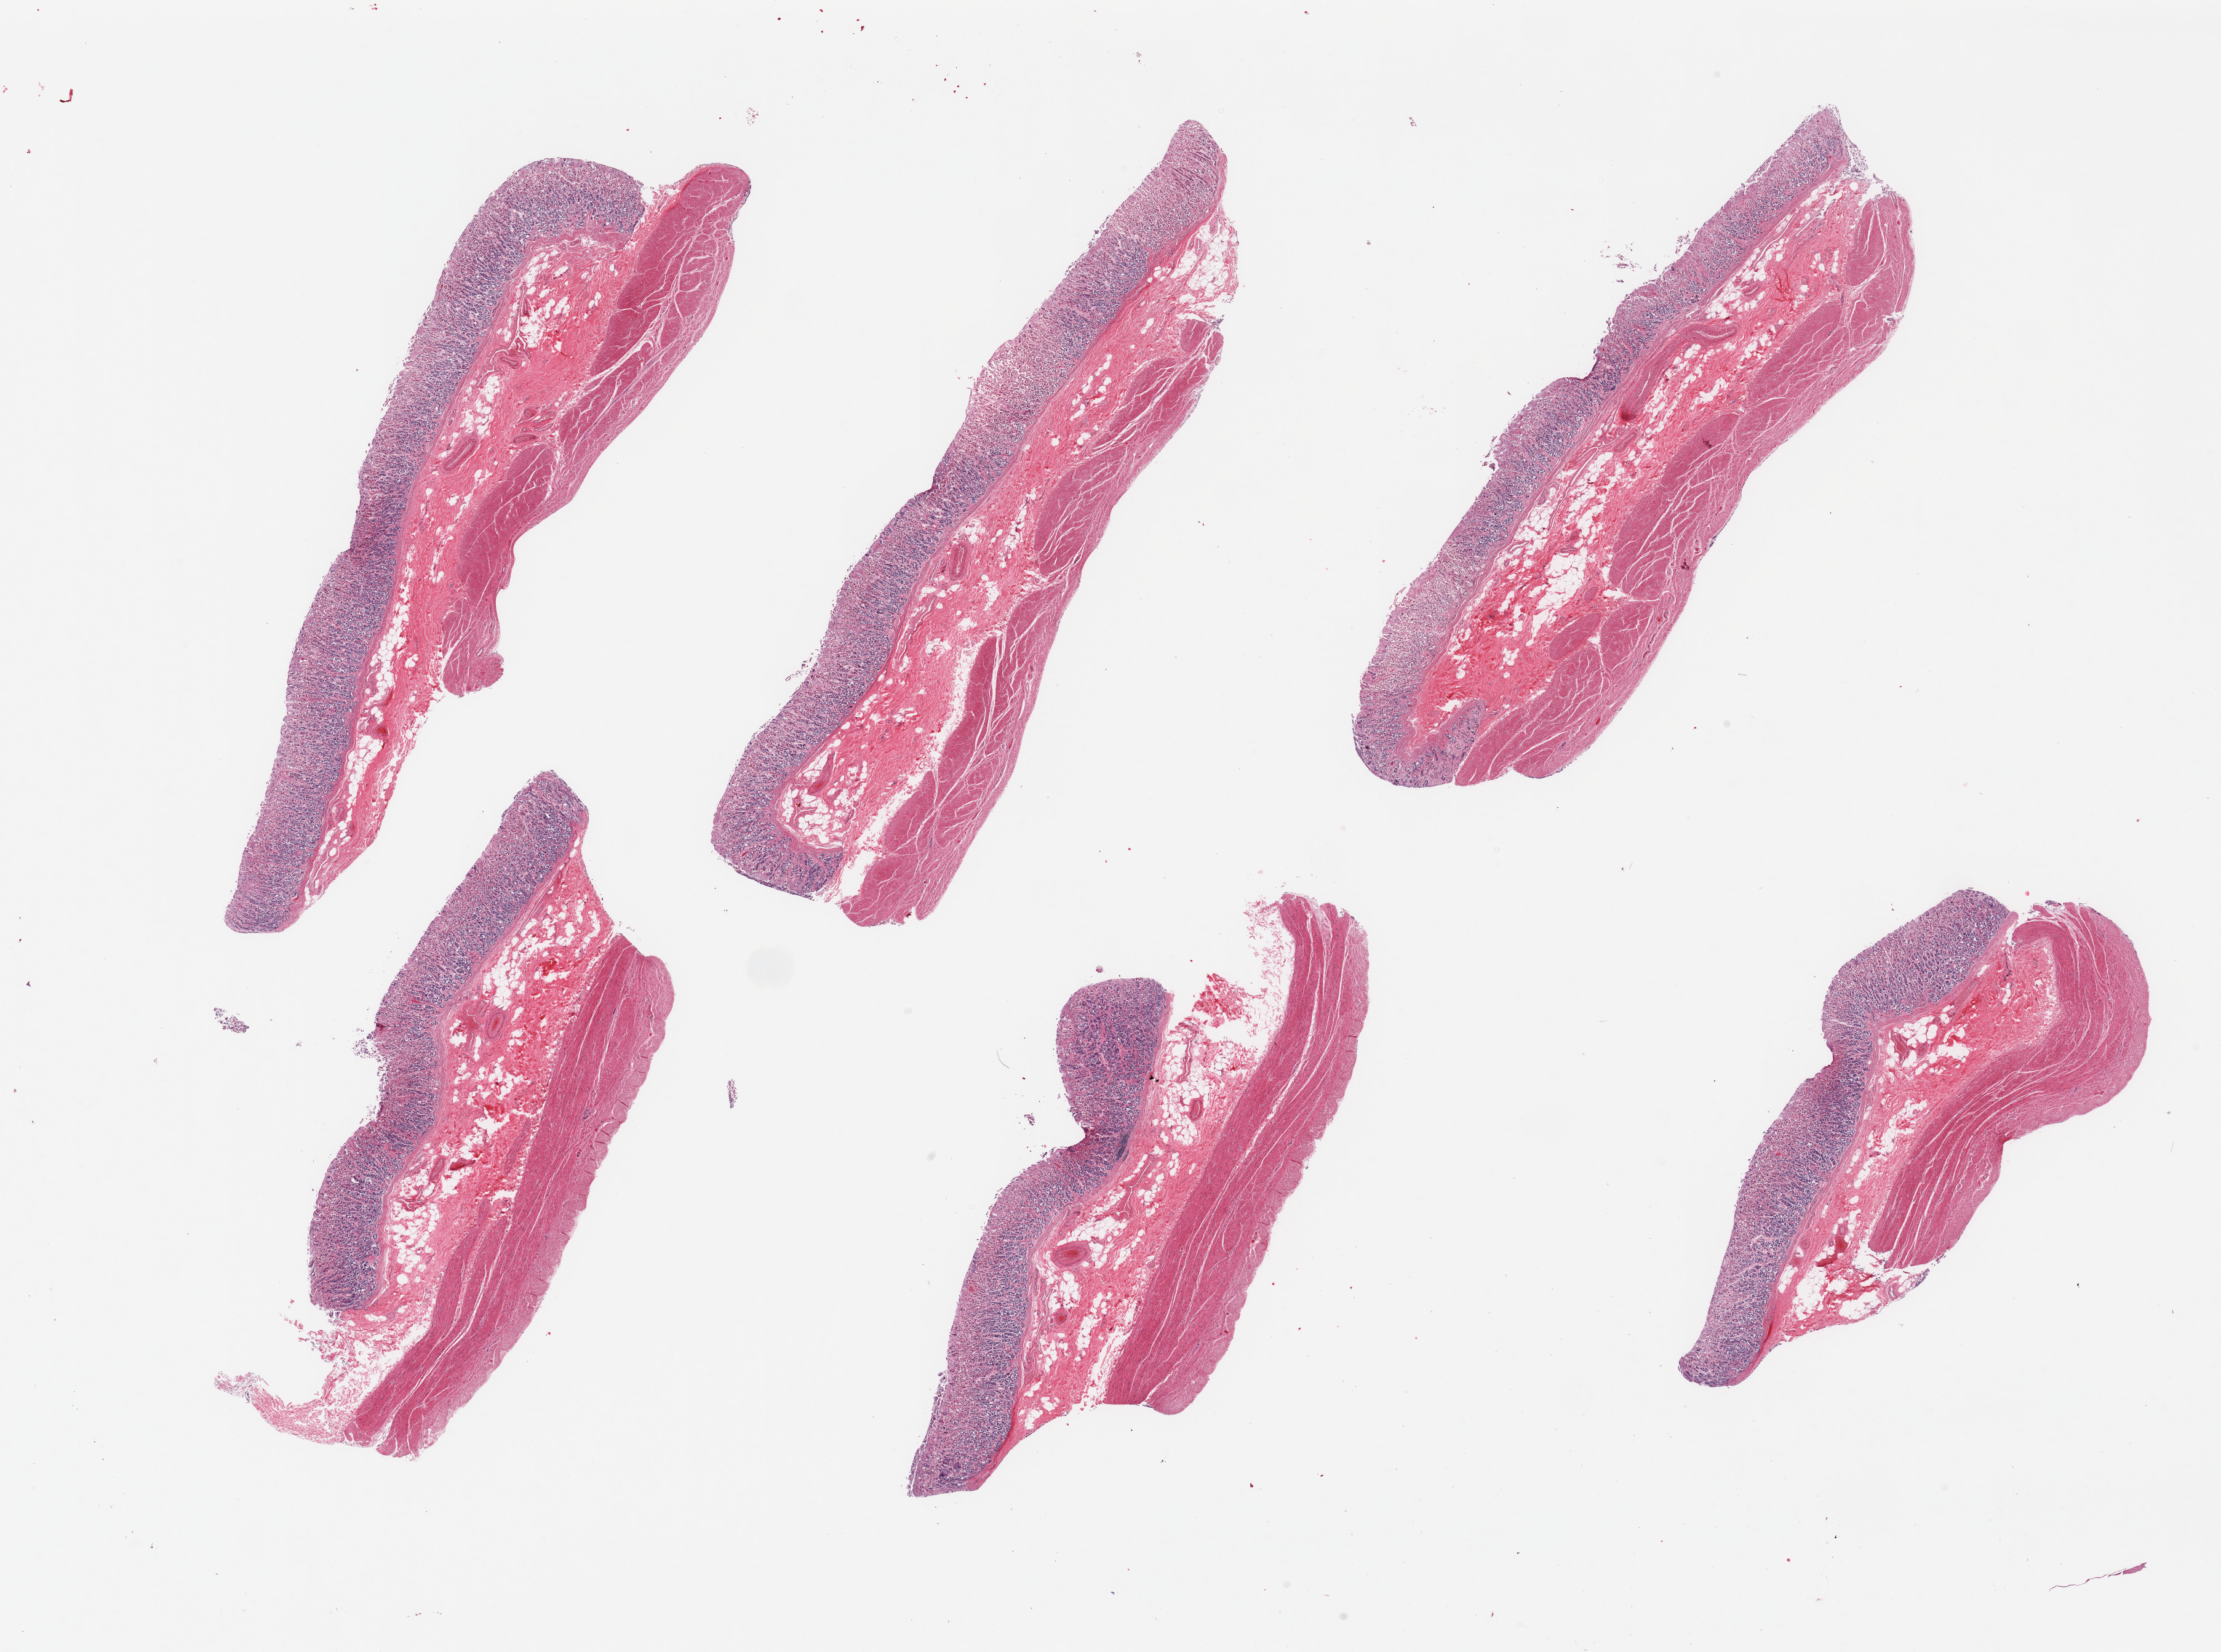
Whole-slide image, haematoxylin and eosin stain, low-resolution overview of the scanned area, about 28.5 x 21.2 mm (acquisition: 20x scan), PAXgene-fixed, paraffin-embedded tissue, sampled site (target tissue): stomach, tissue donor sample. Donor sex: male.
Reviewer comment on this tissue sample: 6 pieces; full thickness sections.